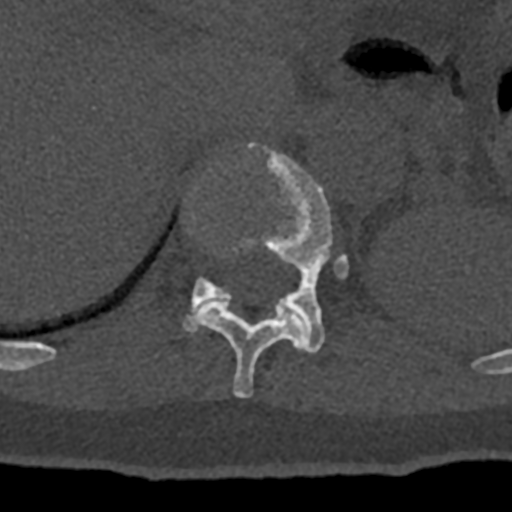
CT including the spine, one axial slice; 120 kVp; bone window (W 1800 / L 400 HU); 512 × 512 image matrix, field of view 160 × 160 mm. Male patient, age 74 years. From the clinical record (not read from this slice): primary cancer: renal; vertebrae with lytic lesions (as recorded): T10, L1, L2, L3, L4, L5.
Annotated regions visible in this slice (semi-automatic segmentation, software-assisted and operator-edited):
- T11 vertebra: bounding box (x1, y1, x2, y2) in pixels: (193, 300, 307, 398)
- T12 vertebra: (183, 142, 349, 354)